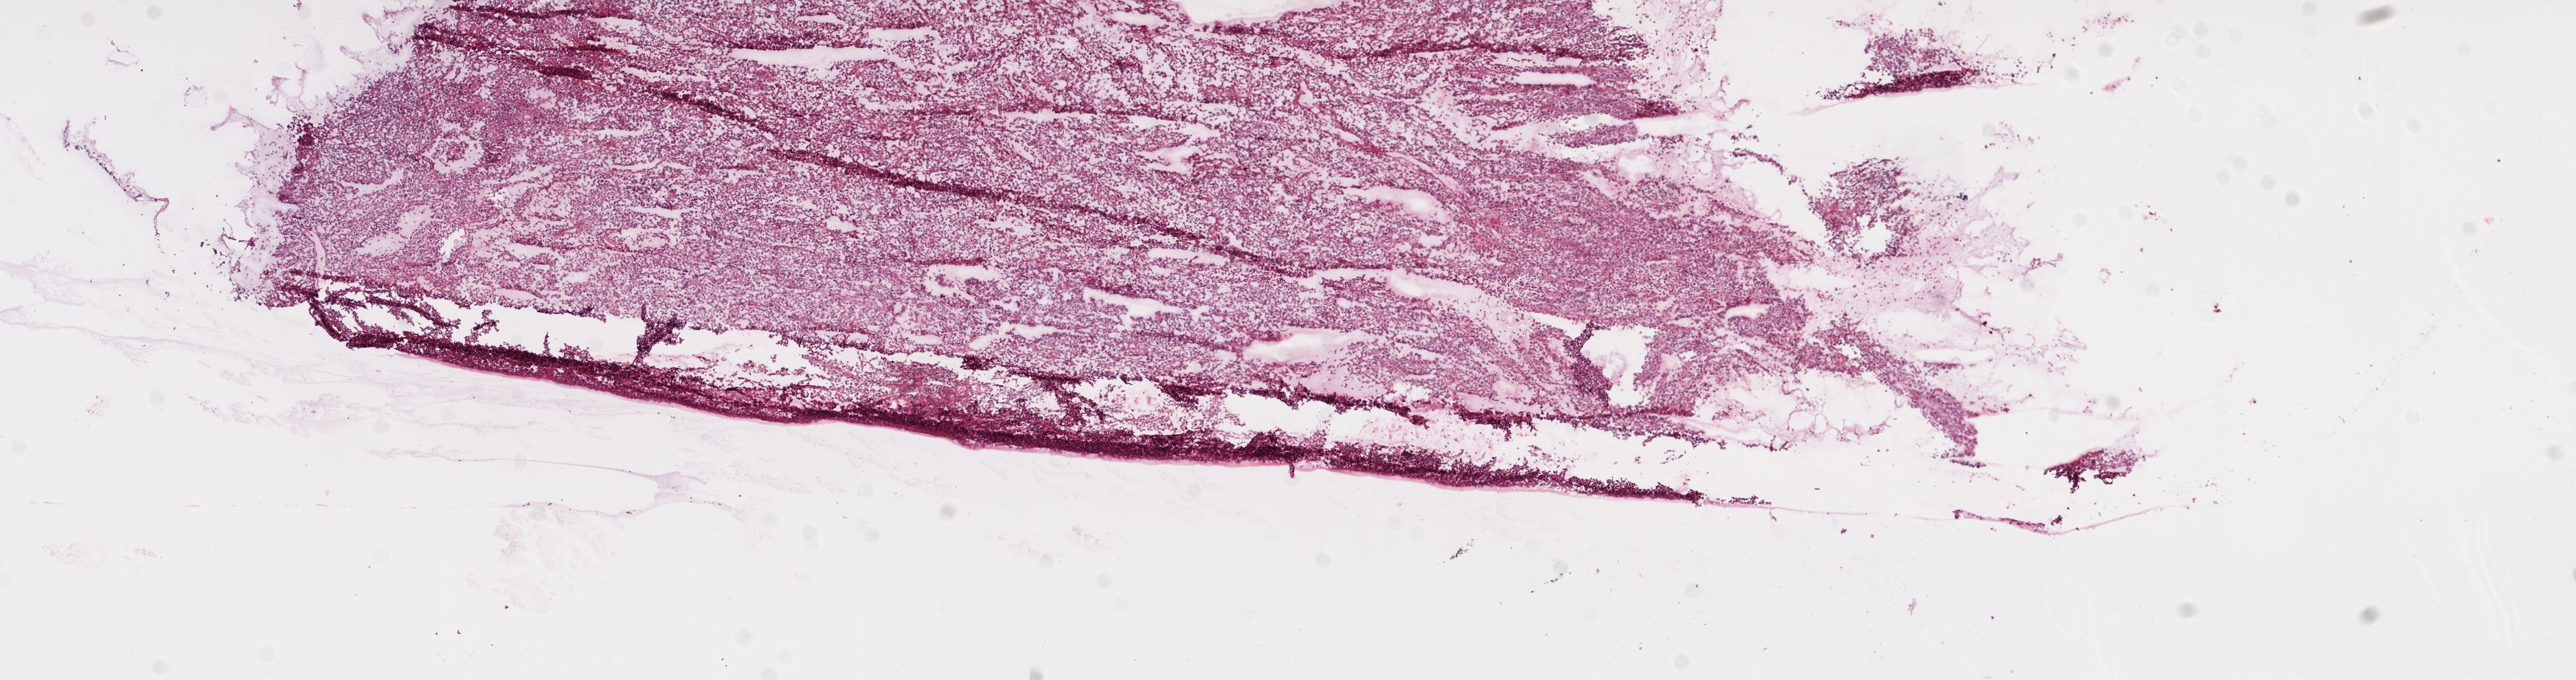
Digitized Hematoxylin and eosin (H&E) stained tissue section (whole slide), low-resolution overview of the scanned area, about 15.0 x 4.0 mm; frozen section from the top of the tissue portion; primary tumour sample from the kidney. Patient: female, age at initial diagnosis 65 years. Histologic grade: G4 (undifferentiated). Composition of this section per pathologist review: tumour cells 95%, tumour nuclei 85%, normal cells 0%, stromal cells 5%, necrosis 0%.
* laterality: right
* AJCC pathologic stage: IV
* pathologic diagnosis: Clear cell adenocarcinoma, NOS